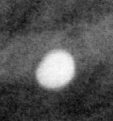
Crop from a digitized film mammogram around one marked abnormality, right breast, MLO view.
Marked abnormality: calcifications, morphology coarse / round and regular / lucent centered; BI-RADS assessment category 2; subtlety rating 4 on a 1 (subtle) to 5 (obvious) scale; benign without callback (not worked up further).